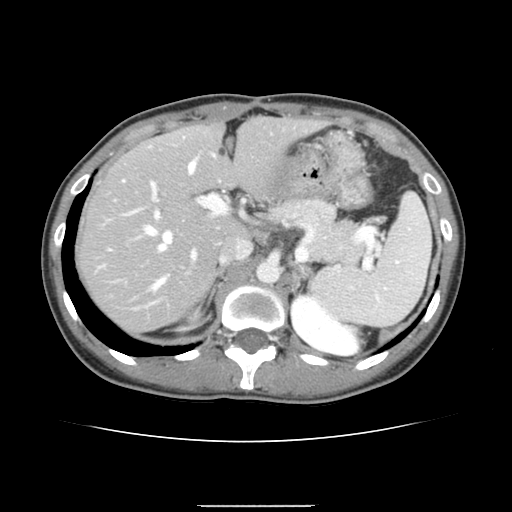
Contrast-enhanced abdominal CT, one axial slice; slice 99 of 150 in the series (ordered by position); intravenous contrast given; soft-tissue window (W 400 / L 40 HU); 2.5 mm slice thickness; 512 × 512 image matrix, field of view 324 × 324 mm. Female patient, age 32 years. From the clinical record (not read from this slice): diagnosis: colorectal cancer liver metastases, imaged before liver resection; multiple liver metastases: yes; largest metastasis: 0.7 cm; disease in both lobes: no.
Outlined on this slice (manually delineated by an expert):
- hepatic veins: bounding box (x1, y1, x2, y2) in pixels: (145, 161, 195, 288)
- liver: (80, 116, 315, 331)
- planned liver remnant (the part of the liver to remain after resection): (79, 116, 316, 281)
- portal vein (with intrahepatic branches): (123, 158, 226, 291)